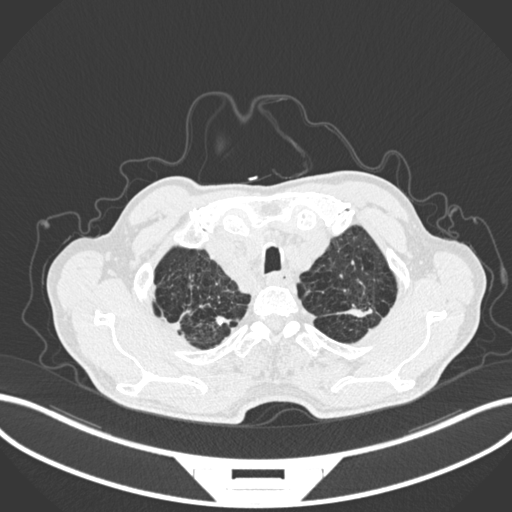
Chest CT, one axial slice. Slice 246 of 287 in the series (ordered by position). Reconstruction kernel B30f. 120 kVp. Lung window (W 1500 / L -600 HU). 1 mm slice thickness. 512 × 512 image matrix, field of view 400 × 400 mm. Male patient, age 74 years. From the clinical record (not read from this slice): clinical TNM (as recorded): T2a N1 M0.
Structures marked on this image (bounding box drawn by a radiologist):
- lung tumour (recorded histology: adenocarcinoma): bounding box (x1, y1, x2, y2) in pixels: (335, 306, 379, 322)